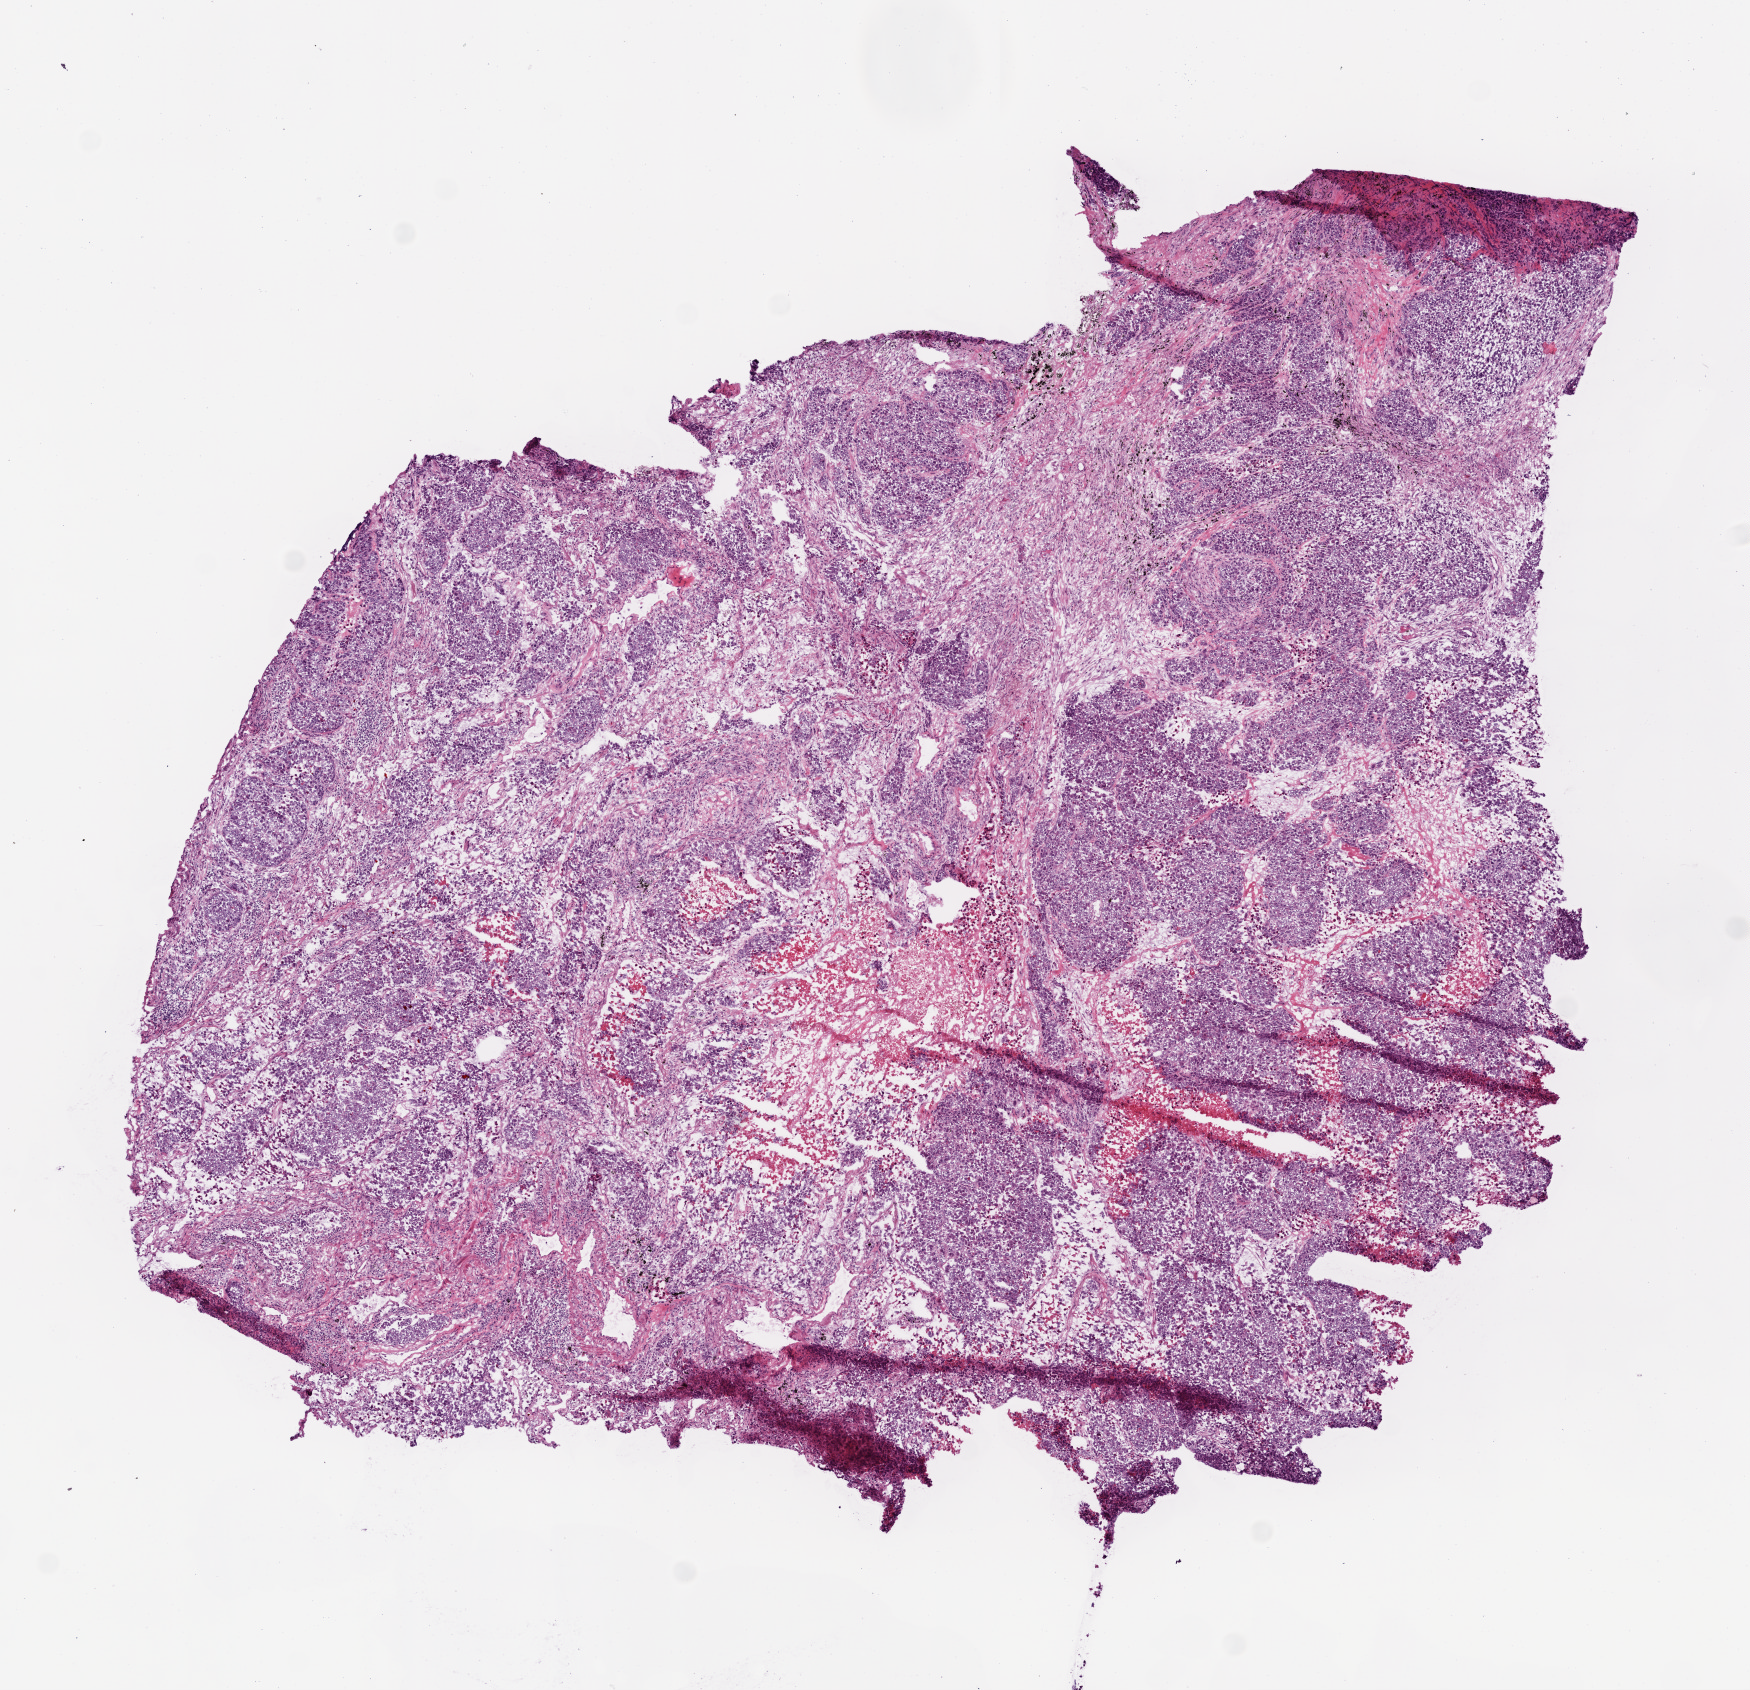
Digitized Hematoxylin and eosin (H&E) stained tissue section (whole slide) — whole scanned area (about 7.0 x 6.8 mm, acquisition: 20x scan) shown as a low-resolution overview. Frozen section from the top of the tissue portion. Lung, primary tumour sample. Male, age 81 years at initial diagnosis. Pathologist review of this section (percent, as recorded): tumour cells 65%, tumour nuclei 75%, stromal cells 20%, necrosis 15%. Inflammatory infiltration, as recorded: lymphocyte infiltration 2%.
Diagnosis: Adenocarcinoma, NOS (upper lobe, lung). TNM: T2 N2 M0. AJCC pathologic stage: IIIA (6th edition).